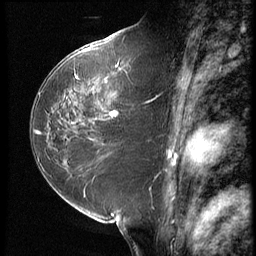
Breast MRI (dynamic contrast-enhanced), one sagittal slice; position 35 of 64 along the scan axis; 3 images stored at this slice position (order not interpretable as contrast timing); 1.5 T; TE 4.2 ms, TR 9 ms; 2.5 mm slice thickness; 256 × 256 image matrix, field of view 180 × 180 mm. Patient: female, 59 years. Case-level facts recorded for this patient, not image findings: setting: breast cancer imaged before/during neoadjuvant chemotherapy; receptor status: HER2-positive.
Annotated regions visible in this slice (semi-automatically segmented with operator editing):
- analysis volume of interest (the breast-tissue region the enhancement analysis was run in; not a lesion): box from (x=54, y=65) to (x=155, y=132) px
- tumour enhancement mask (voxels above the 140 % enhancement threshold inside the analysis volume of interest): (x=65, y=65)–(x=122, y=121)